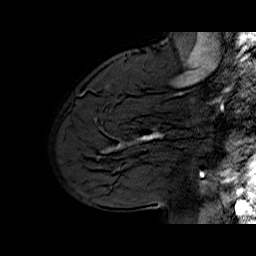
Breast MRI (dynamic contrast-enhanced), one sagittal slice; dynamic contrast-enhanced series, time point 2 of 6 at this slice position (early post-contrast); 1.5 T; TE 6.5 ms, TR 33 ms; 4 mm slice thickness; 256 × 256 image matrix, field of view 200 × 200 mm. Female patient. Case-level facts recorded for this patient, not image findings: setting: breast cancer imaged before/during neoadjuvant chemotherapy; receptor status: HER2-positive.
Outlined on this slice (semi-automatic segmentation, software-assisted and operator-edited):
- analysis volume of interest (the breast-tissue region the enhancement analysis was run in; not a lesion): bounding box (x1, y1, x2, y2) in pixels: (113, 112, 174, 170)
- tumour enhancement mask (voxels above the 100 % enhancement threshold inside the analysis volume of interest): (120, 134, 158, 145)